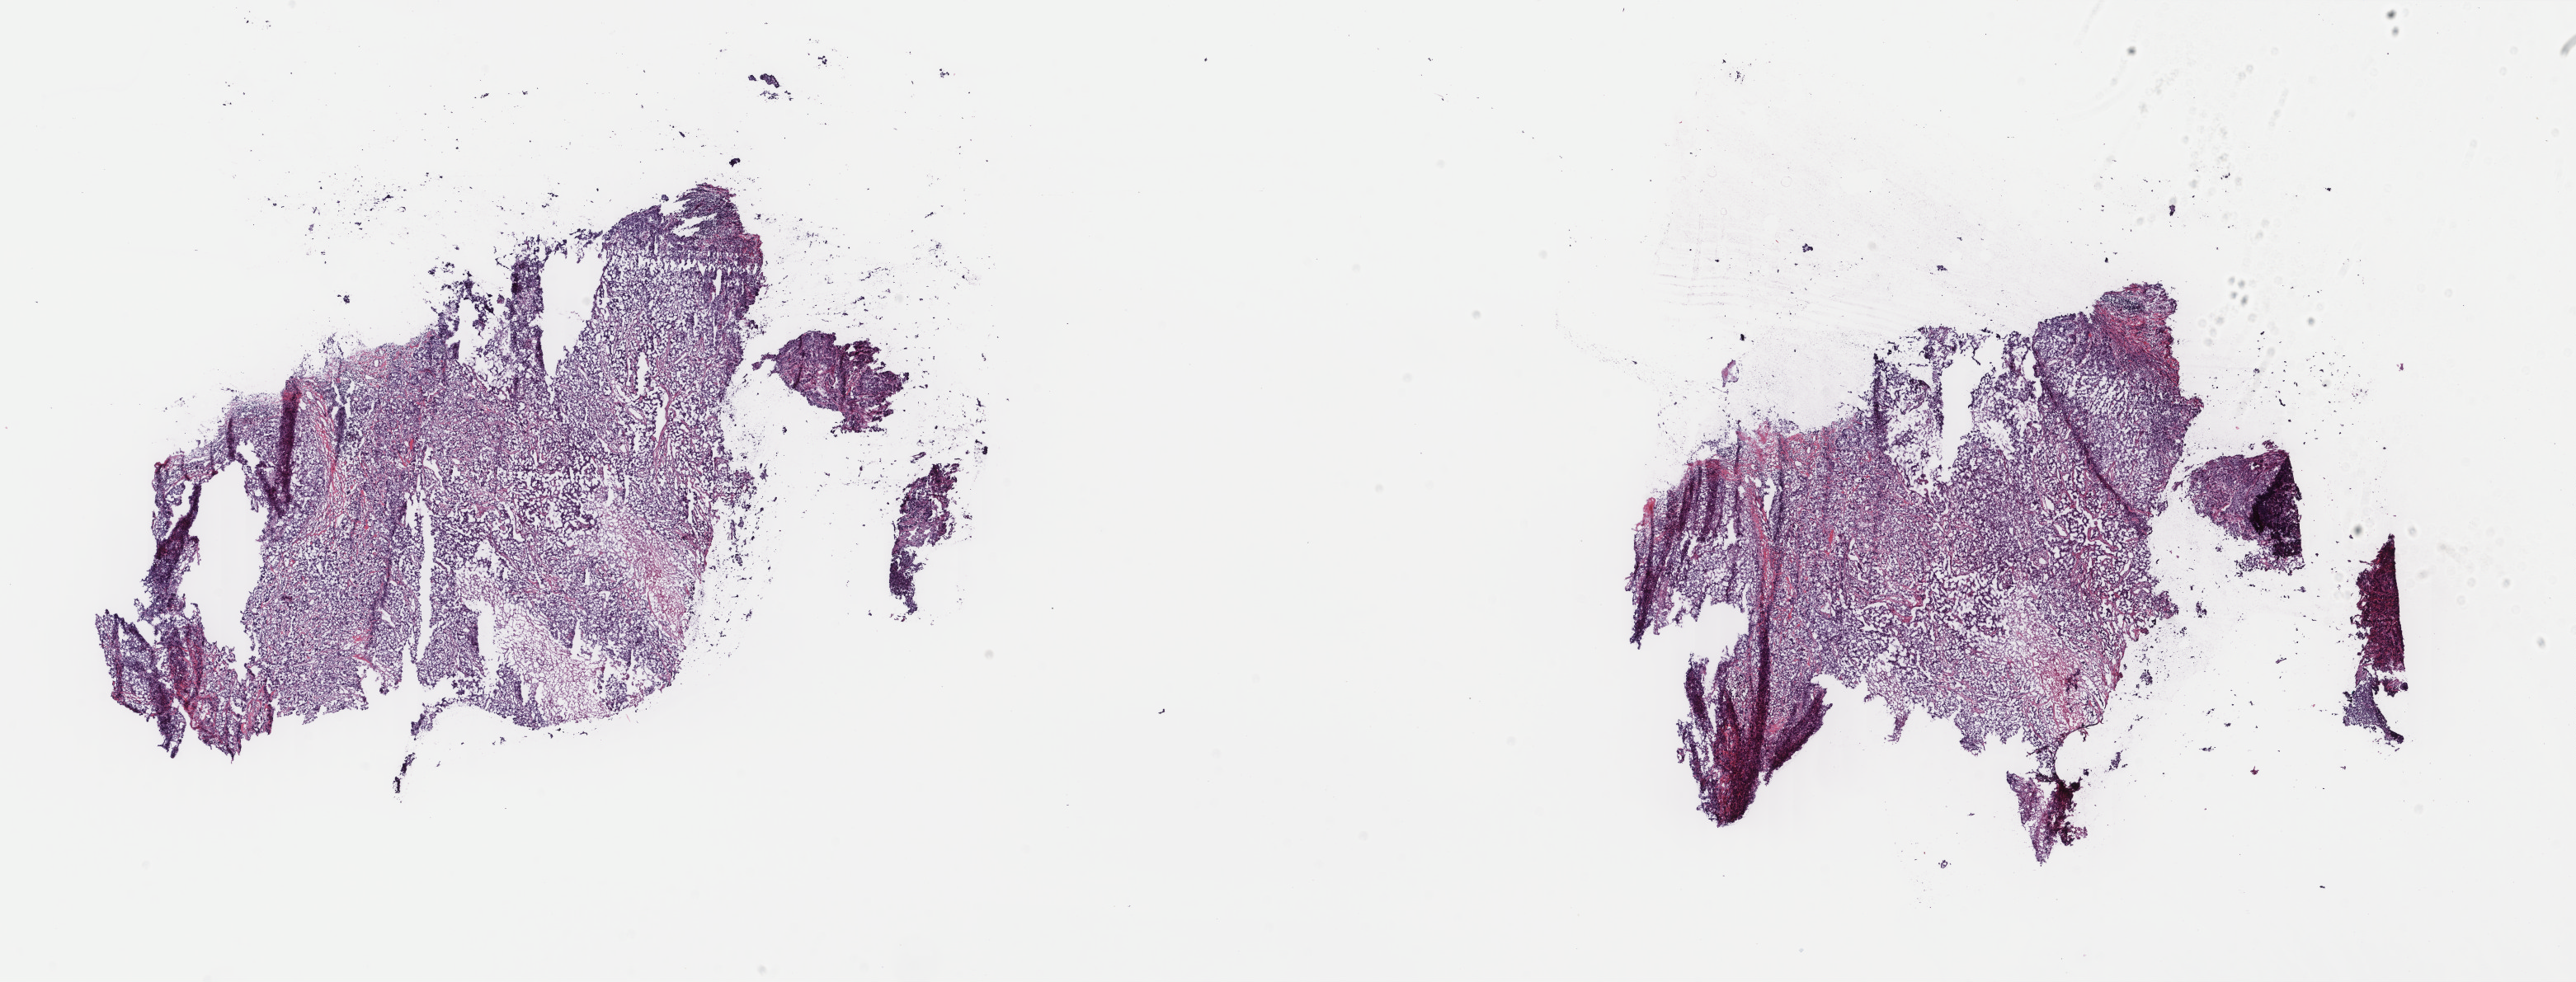
Digitized H&E-stained tissue section (whole slide) — shown as a low-resolution overview of the whole scanned area (about 24.8 x 9.5 mm, slide scanned at 40x), frozen section from the bottom of the tissue portion, breast, primary tumour sample. Female patient; age at initial diagnosis 29 years. Slide review estimates, as recorded: tumour cells 85%, tumour nuclei 70%, normal cells 0%, stromal cells 0%, necrosis 15%. Infiltration values recorded for this section: lymphocyte infiltration 0%, monocyte infiltration 0%, neutrophil infiltration 0%.
TNM: T2 N1a M0. Lymph nodes positive (case pathology): 2 of 21 examined. AJCC pathologic stage: IIB (5th edition). Histologic diagnosis: Infiltrating duct carcinoma, NOS.